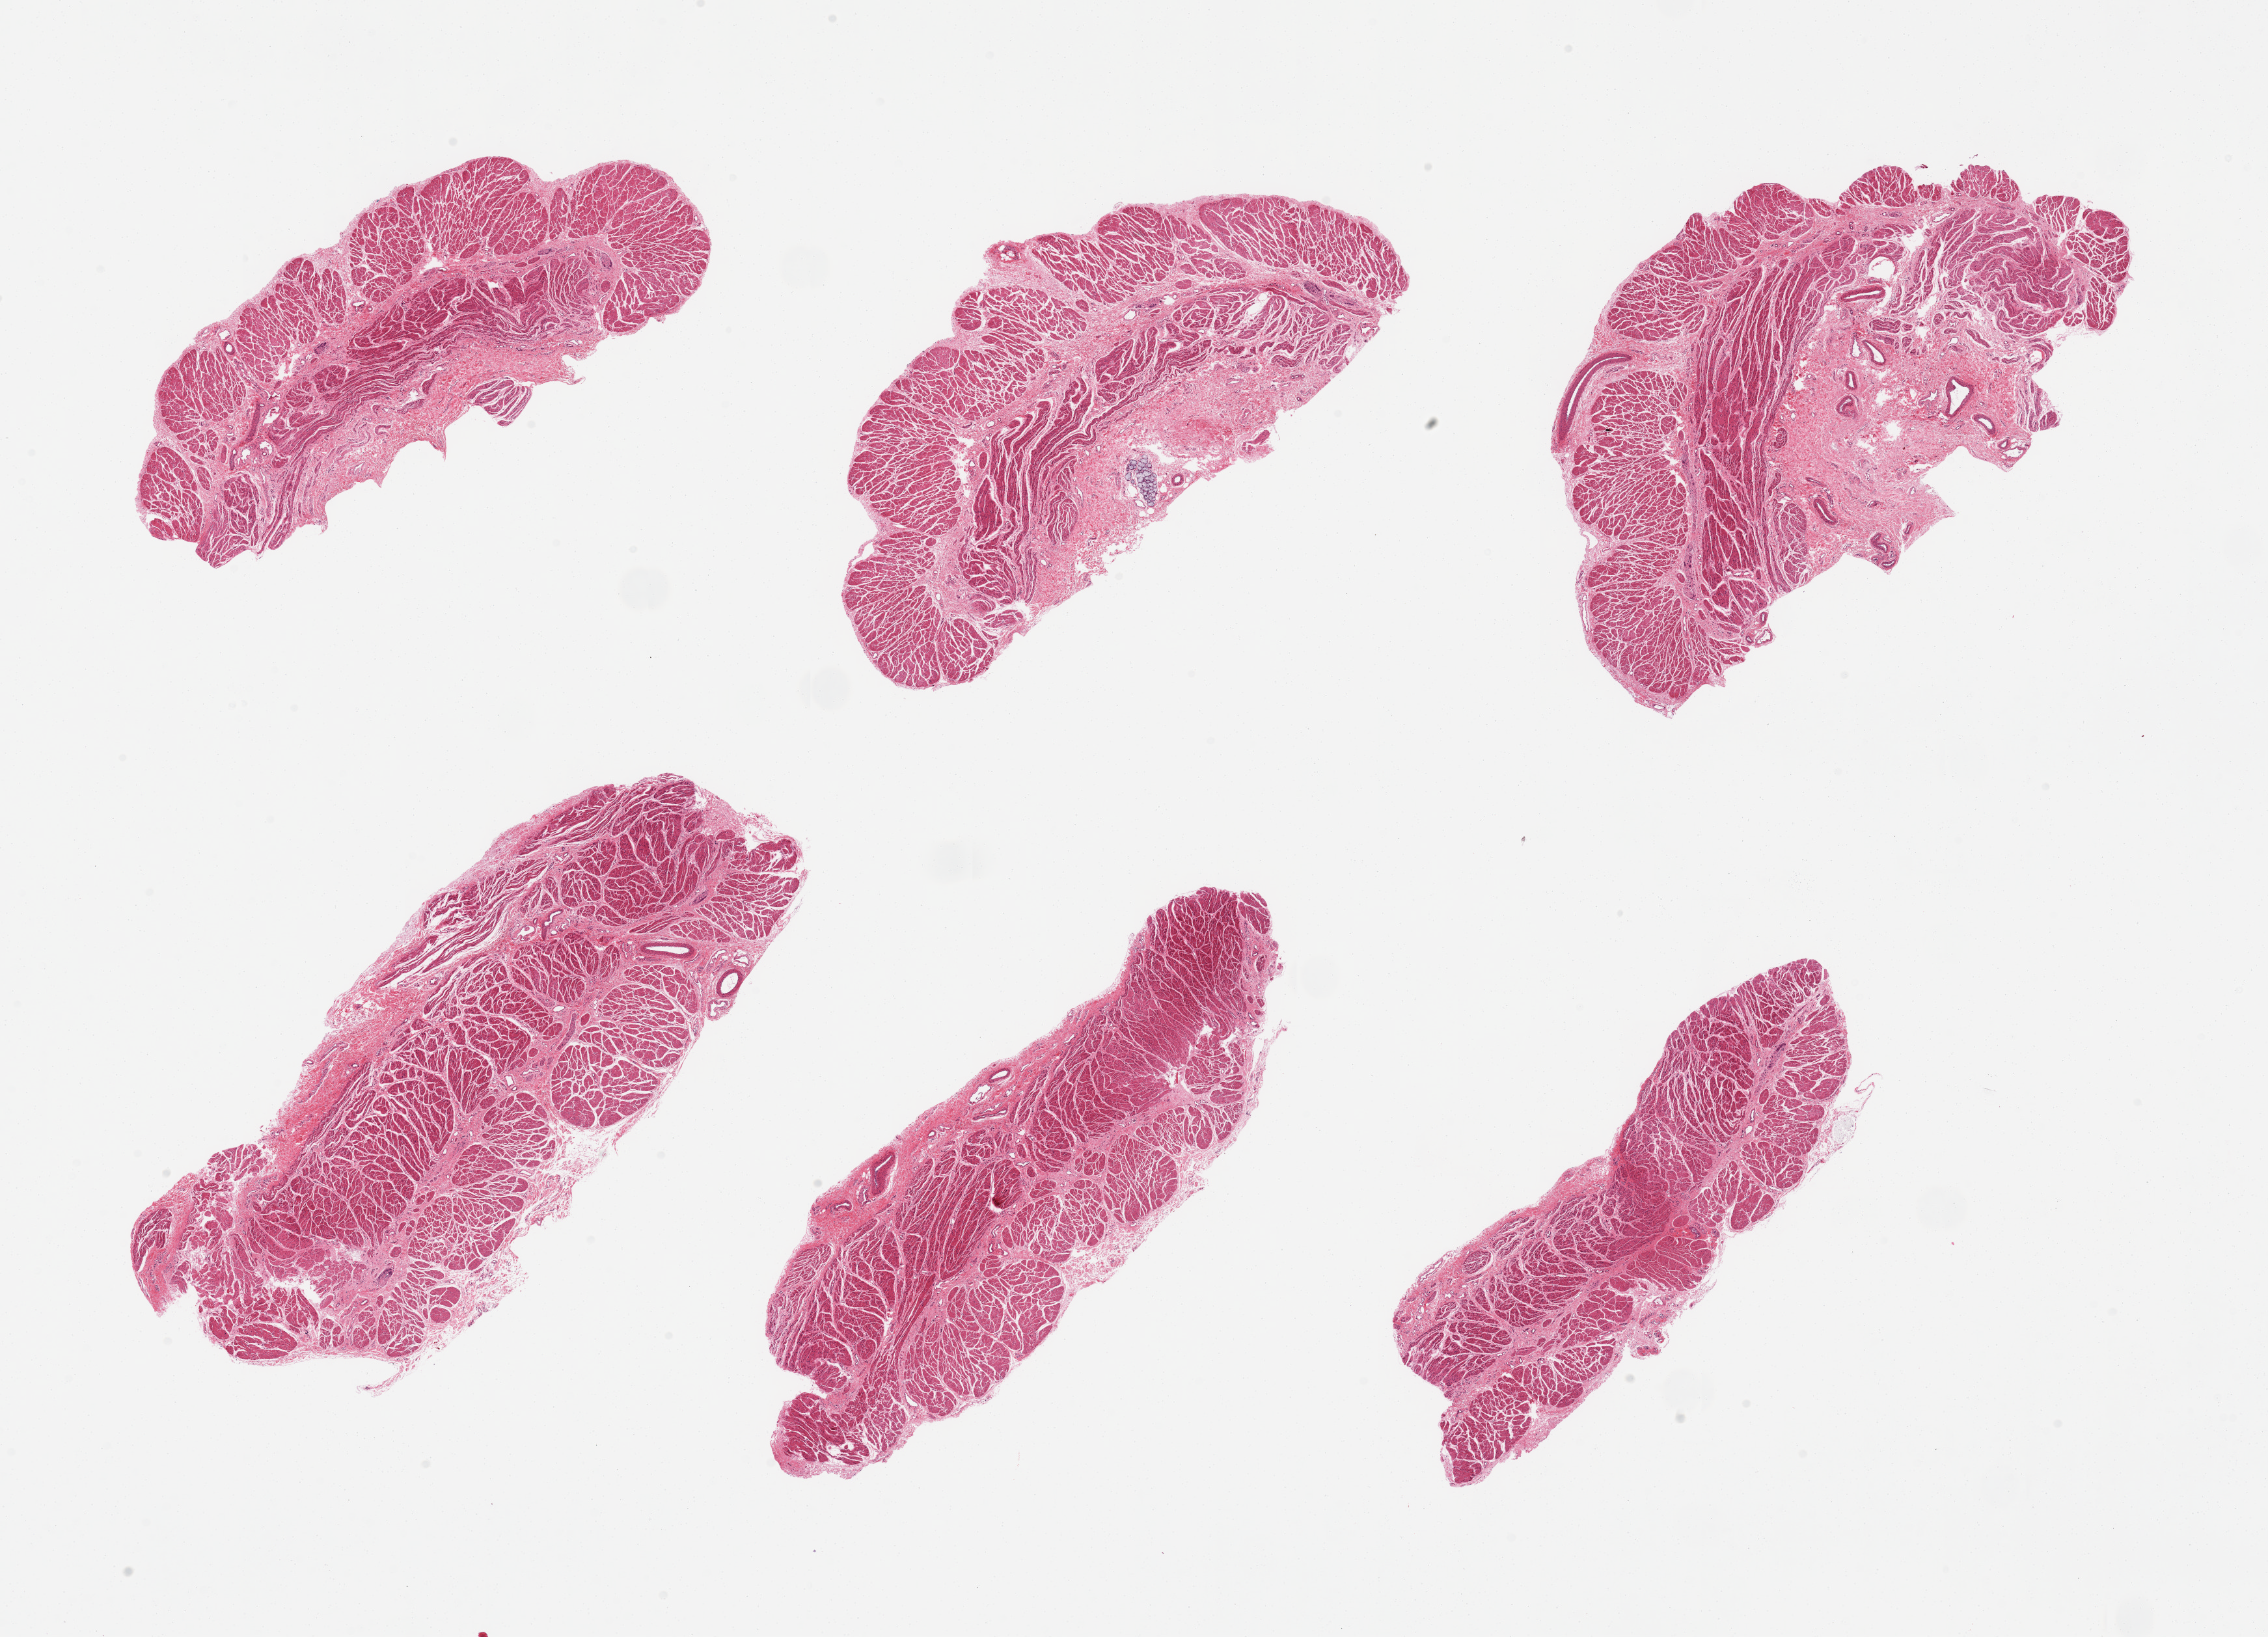
Digitized haematoxylin and eosin-stained section — whole scanned area (about 27.6 x 19.9 mm, slide scanned at 20x) shown as a low-resolution overview. PAXgene-fixed, paraffin-embedded tissue. Target tissue: gastroesophageal junction. Donor tissue sample. Donor sex: male.
Reviewer comment on this tissue sample: 6 pieces, well trimmed, rare group of submucosal glands.